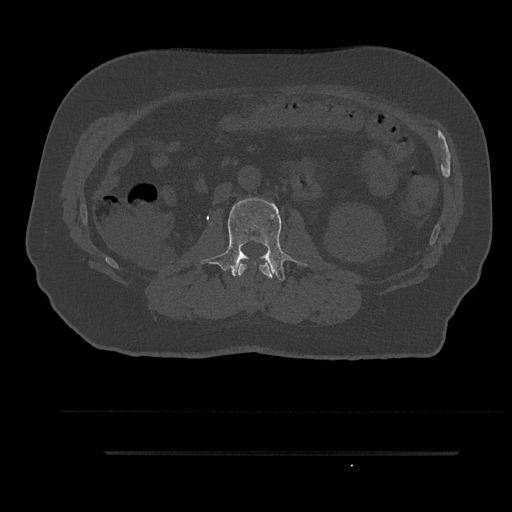
CT including the spine, one axial slice. Reconstruction kernel Br40s/3. 120 kVp. Bone window (W 1800 / L 400 HU). 0.5 mm slice thickness. 512 × 512 image matrix, field of view 432 × 432 mm. Male patient, age 63 years. Case-level facts recorded for this patient, not image findings: primary cancer: renal.
Structures marked on this image (semi-automatic segmentation, software-assisted and operator-edited):
- L1 vertebra: bounding box (x1, y1, x2, y2) in pixels: (238, 259, 274, 279)
- L2 vertebra: (199, 198, 307, 281)